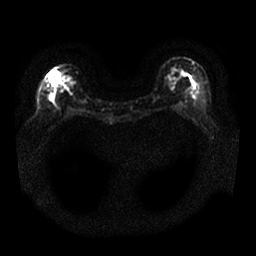
Breast MRI, one axial slice. Slice 10 of 25 in the series (ordered by position). Diffusion-weighted series; image 2 of 4 stored at this slice position (different b-values; order by instance number). 1.5 T. 256 × 256 image matrix, field of view 340 × 340 mm. Female patient.
Annotated regions visible in this slice (manually delineated by an expert):
- tumour on diffusion-weighted imaging: bounding box [x1, y1, x2, y2] px = [49, 70, 60, 83]